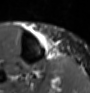
MRI of an extremity soft-tissue mass, one axial slice. STIR. MR volume resampled by the dataset authors to the PET/CT grid (not the native acquisition matrix). 3.27 mm slice thickness. 90 × 93 image matrix, field of view 88 × 91 mm. Female patient. From the clinical record (not read from this slice): histological type: undifferentiated – high grade; grade: high; site of the primary tumour: right thigh.
Outlined on this slice (expert contour drawn on MRI and transferred to this co-registered scan by the dataset authors):
- gross tumour volume (mass): bounding box <35,30,59,56> (left, top, right, bottom; pixels)